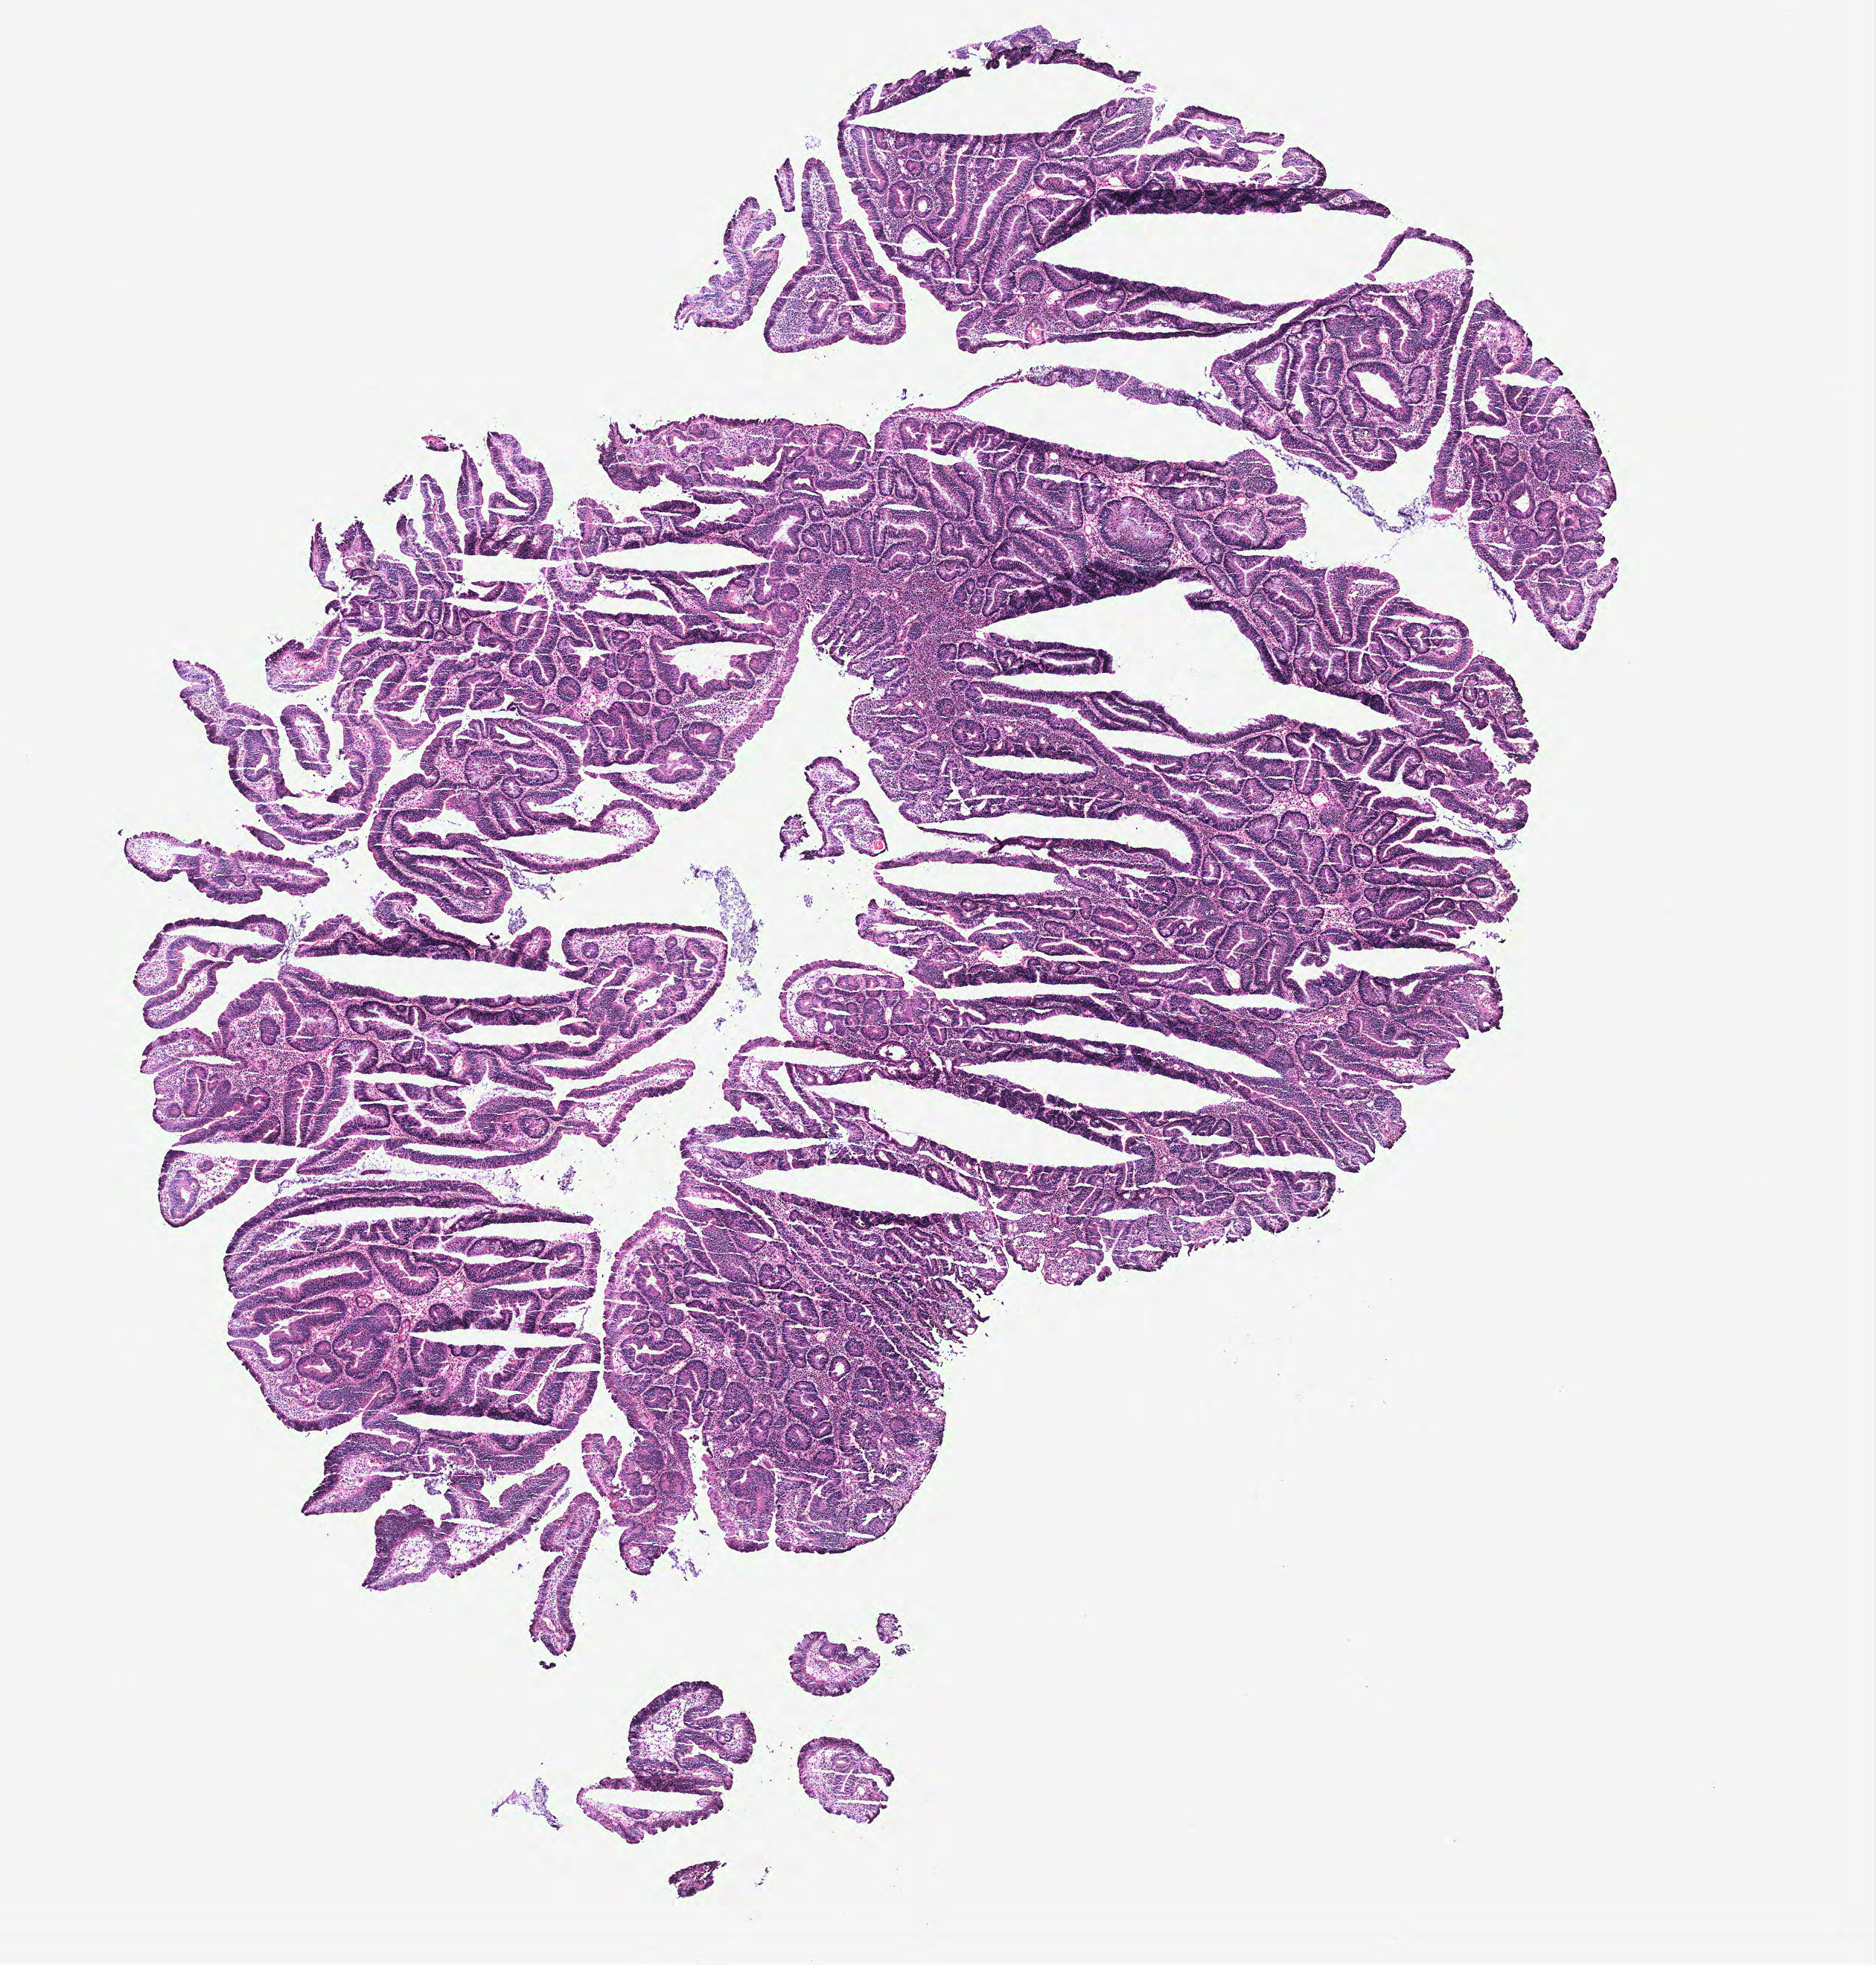
H&E whole-slide image — whole scanned area (about 10.1 x 10.6 mm) shown as a low-resolution overview; colon, normal (non-tumour) tissue. Patient: male, age 86 years.
This section: normal (non-tumour) tissue from the same patient. Patient diagnosis: Adenocarcinoma, NOS.